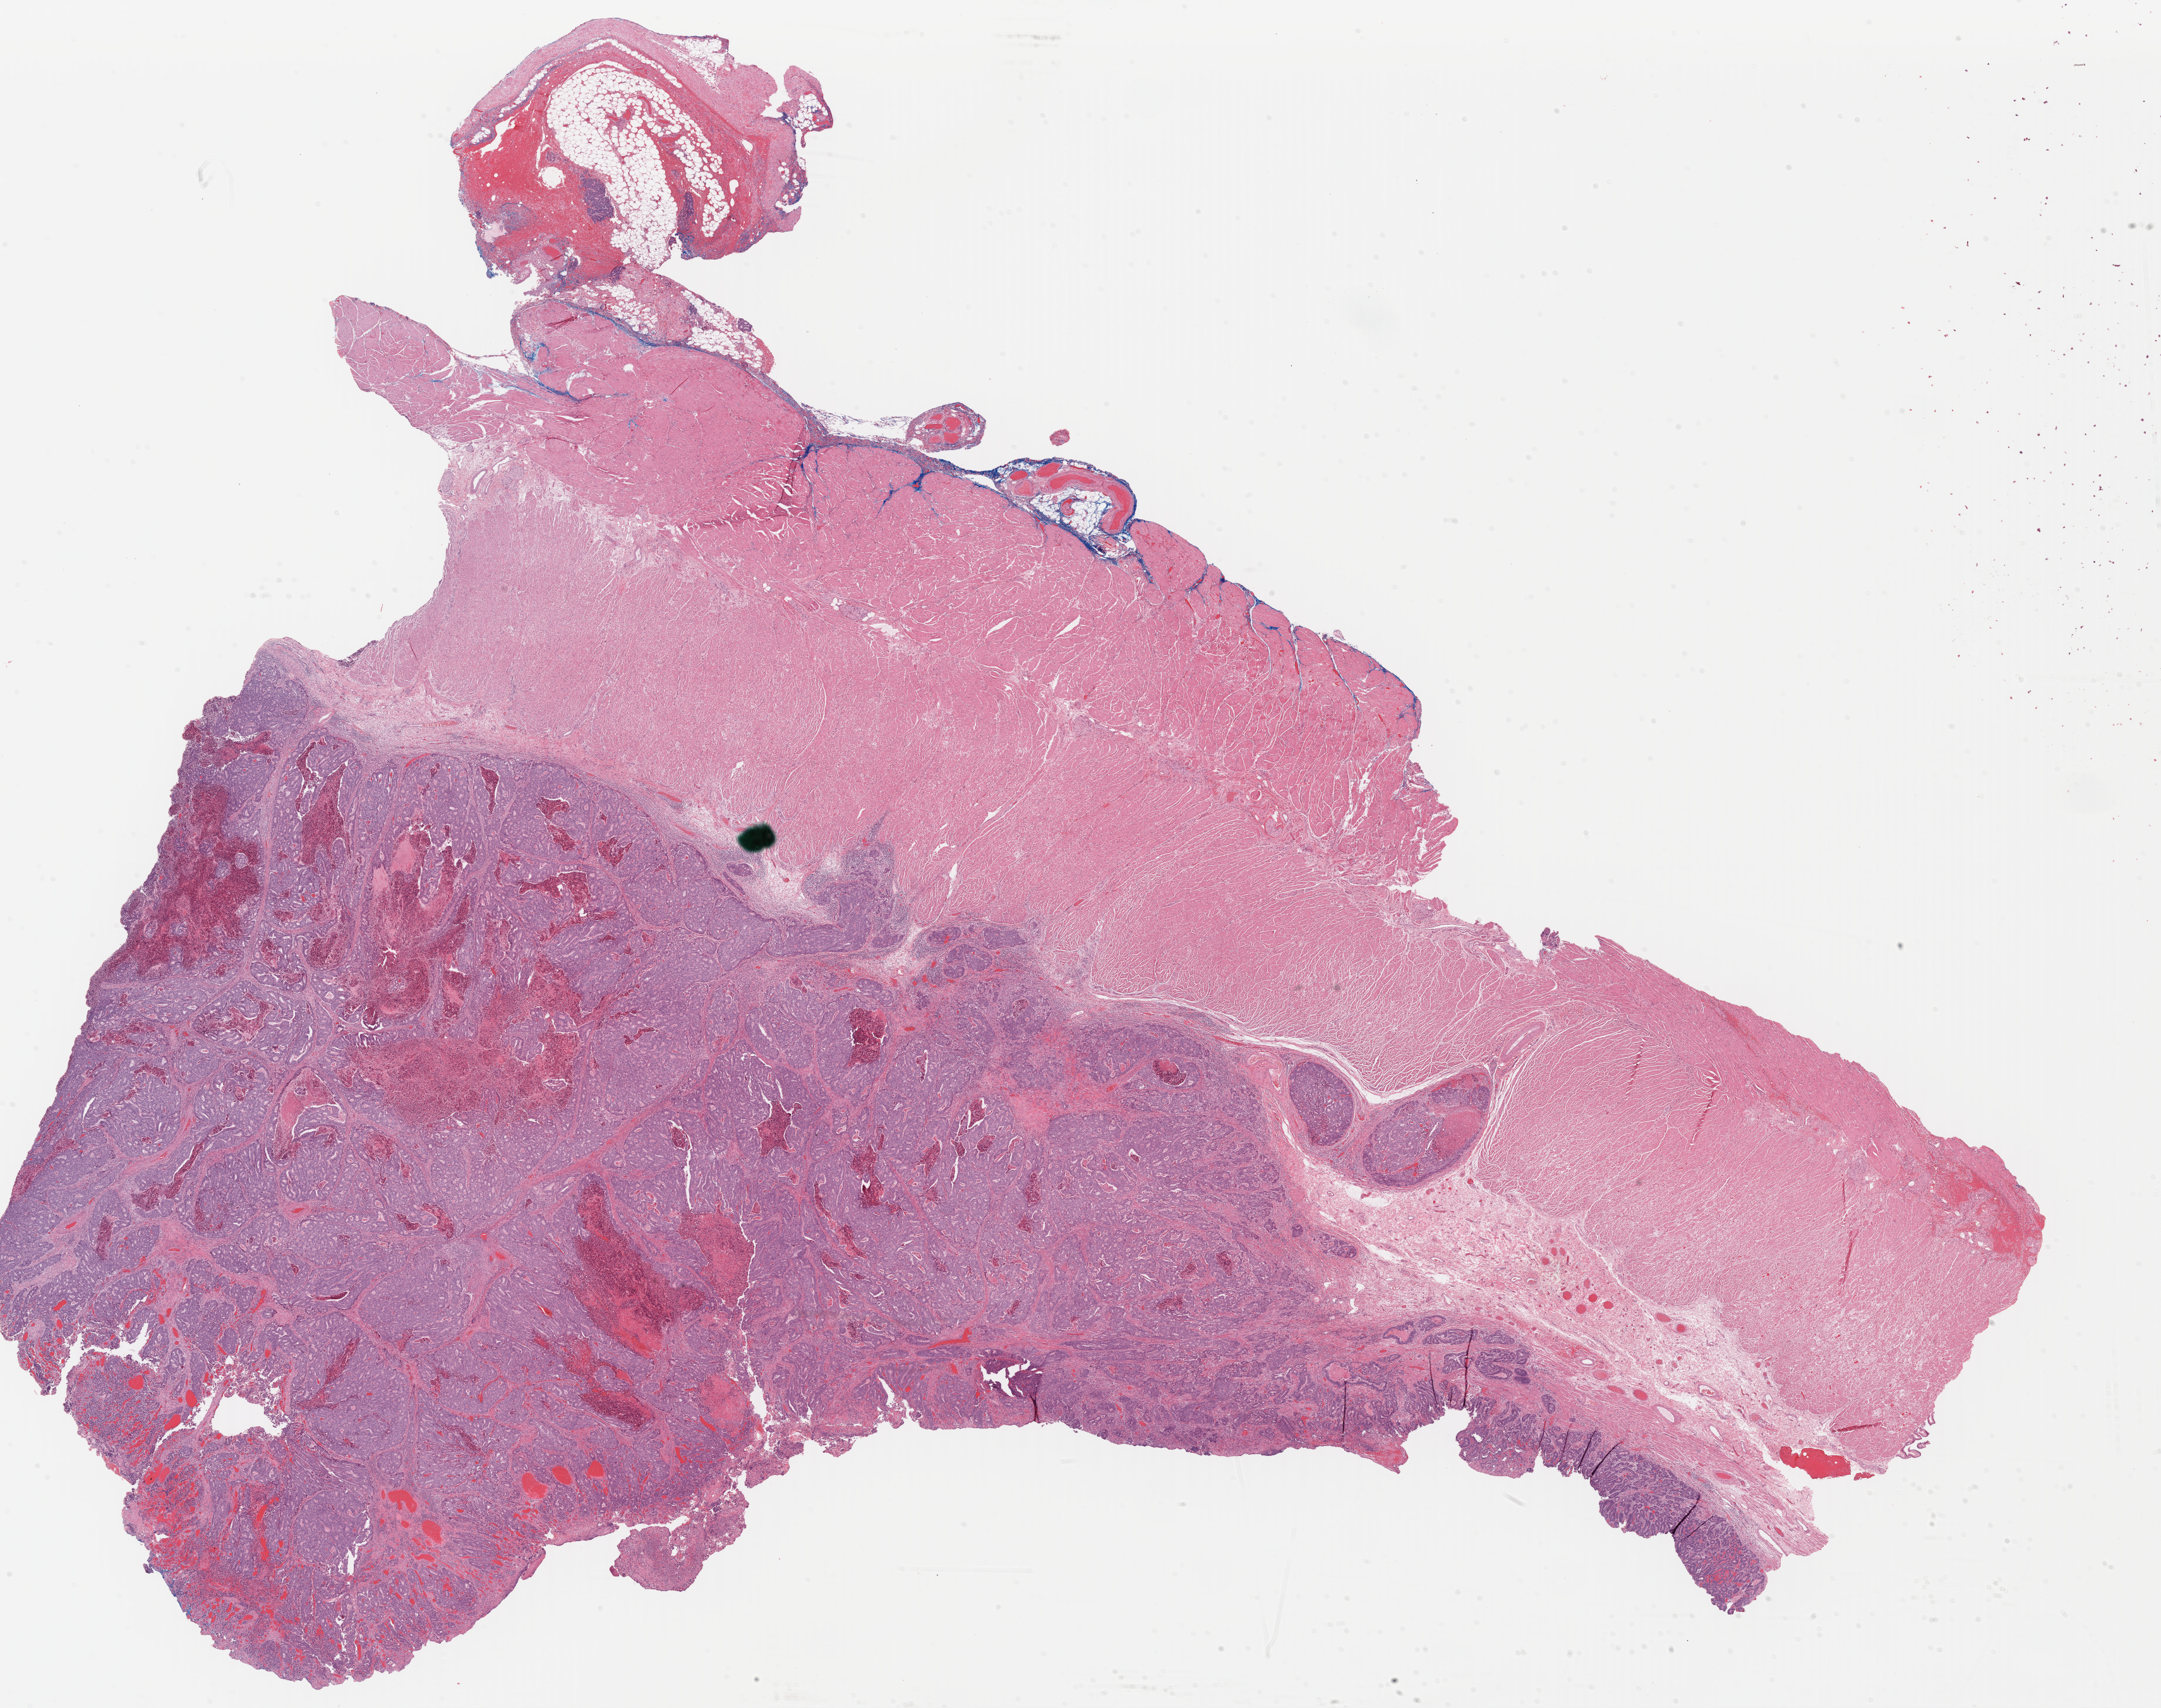
Digitized Hematoxylin and eosin (H&E) stained tissue section (whole slide) — low-resolution overview of the scanned area, about 26.9 x 21.3 mm (slide scanned at 40x); formalin-fixed paraffin-embedded (FFPE) diagnostic section; primary tumour sample from the esophagus. Male, age 60 years at initial diagnosis. Histologic grade: GX (grade cannot be assessed).
AJCC pathologic stage: IIB (6th edition). Pathologic diagnosis: Adenocarcinoma, NOS (lower third of esophagus). Lymph nodes positive (case pathology): 3 of 15 examined.